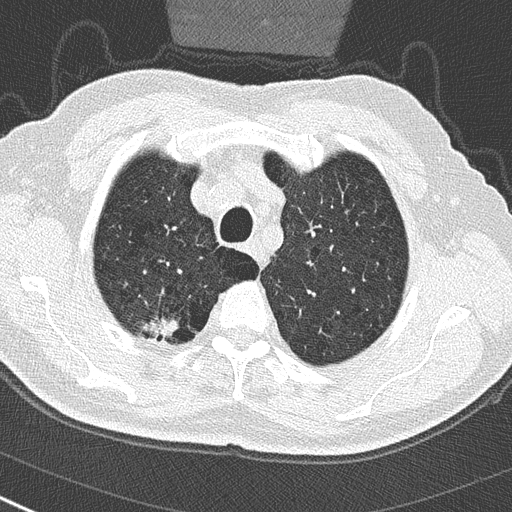
Axial slice from a low-dose chest CT screening exam, baseline annual screen, lung window (W 1500 / L -600 HU), 2 mm slice thickness, slice 50 of 290 in the series. Male, age 65 years at enrolment.
• Lesion marked by an expert reader, box from (x=136, y=304) to (x=183, y=351) px.
• Screening reader's record for this exam (one nodule recorded; not confirmed to be the boxed lesion): non-calcified nodule or mass ≥4 mm, right upper lobe, 24 × 19 mm, spiculated (stellate) margins, soft tissue attenuation.